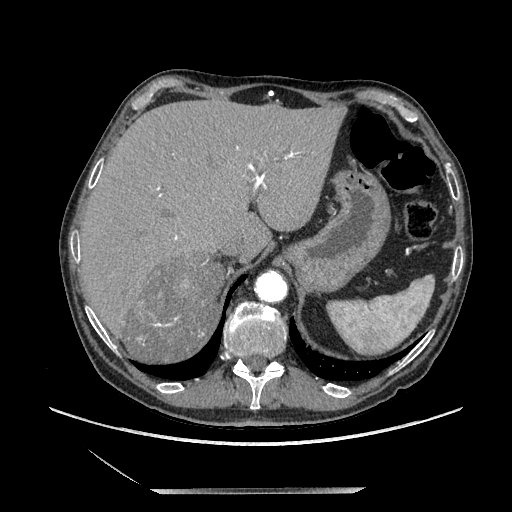
Contrast-enhanced abdominal CT, one axial slice. Position 166 of 243 along the scan axis. Soft-tissue window (W 400 / L 40 HU). 1.25 mm slice thickness. 512 × 512 image matrix, field of view 420 × 420 mm. Male patient. Case-level facts recorded for this patient, not image findings: diagnosis: adrenocortical carcinoma; tumour side: right adrenal; tumour size at pathology: 16 cm; Ki-67 index: 17 %; stage (as recorded): 3.
Annotated regions visible in this slice (semi-automatically segmented with operator editing):
- mass: box from (x=129, y=256) to (x=225, y=362) px